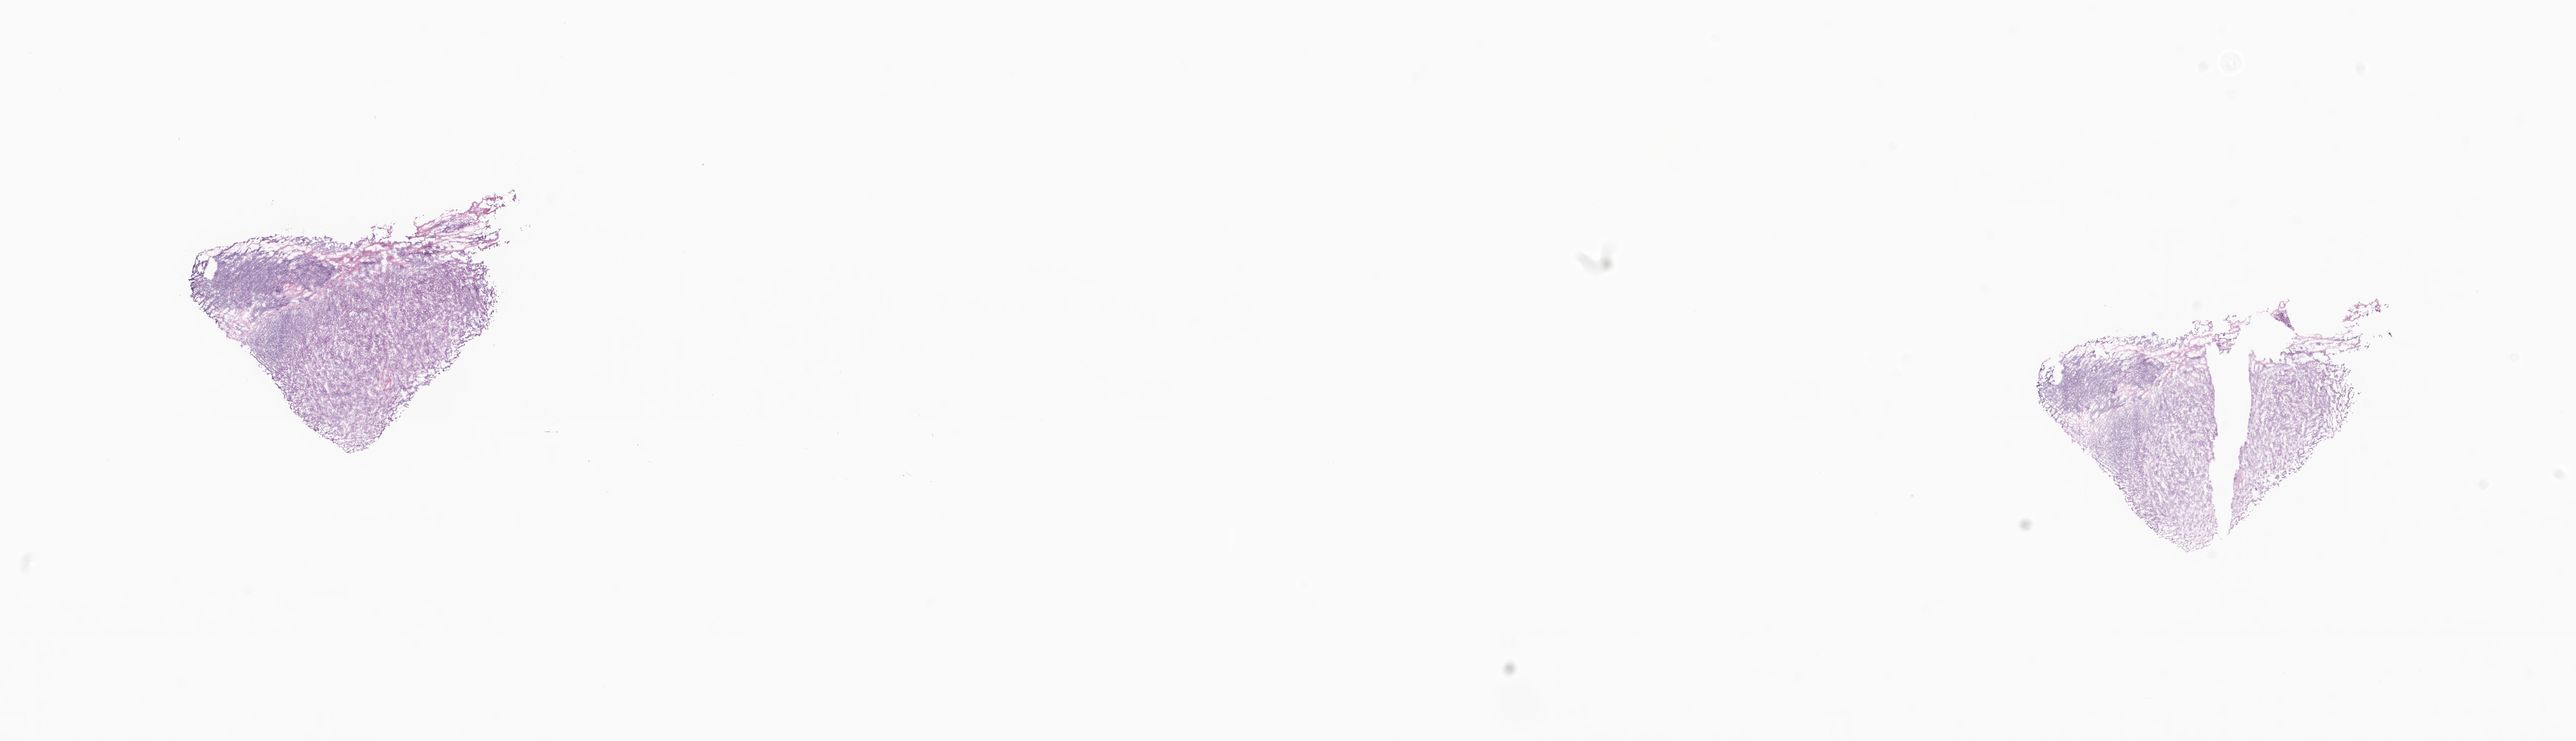
Whole-slide image, hematoxylin and eosin (H&E) stain, low-resolution overview of the scanned area, about 25.5 x 7.3 mm, cryosection, metastatic tumor tissue. Female, age 78 years at initial diagnosis. Composition of this section per pathologist review: tumor cells 90%, tumor nuclei 93%, stromal cells 7%, necrosis 3%, normal cells 0%. Infiltration values recorded for this section: lymphocyte infiltration 13%, monocyte infiltration 0%, neutrophil infiltration 0%.
* patient diagnosis (primary): Infiltrating duct carcinoma, NOS
* section: bottom of the tissue portion